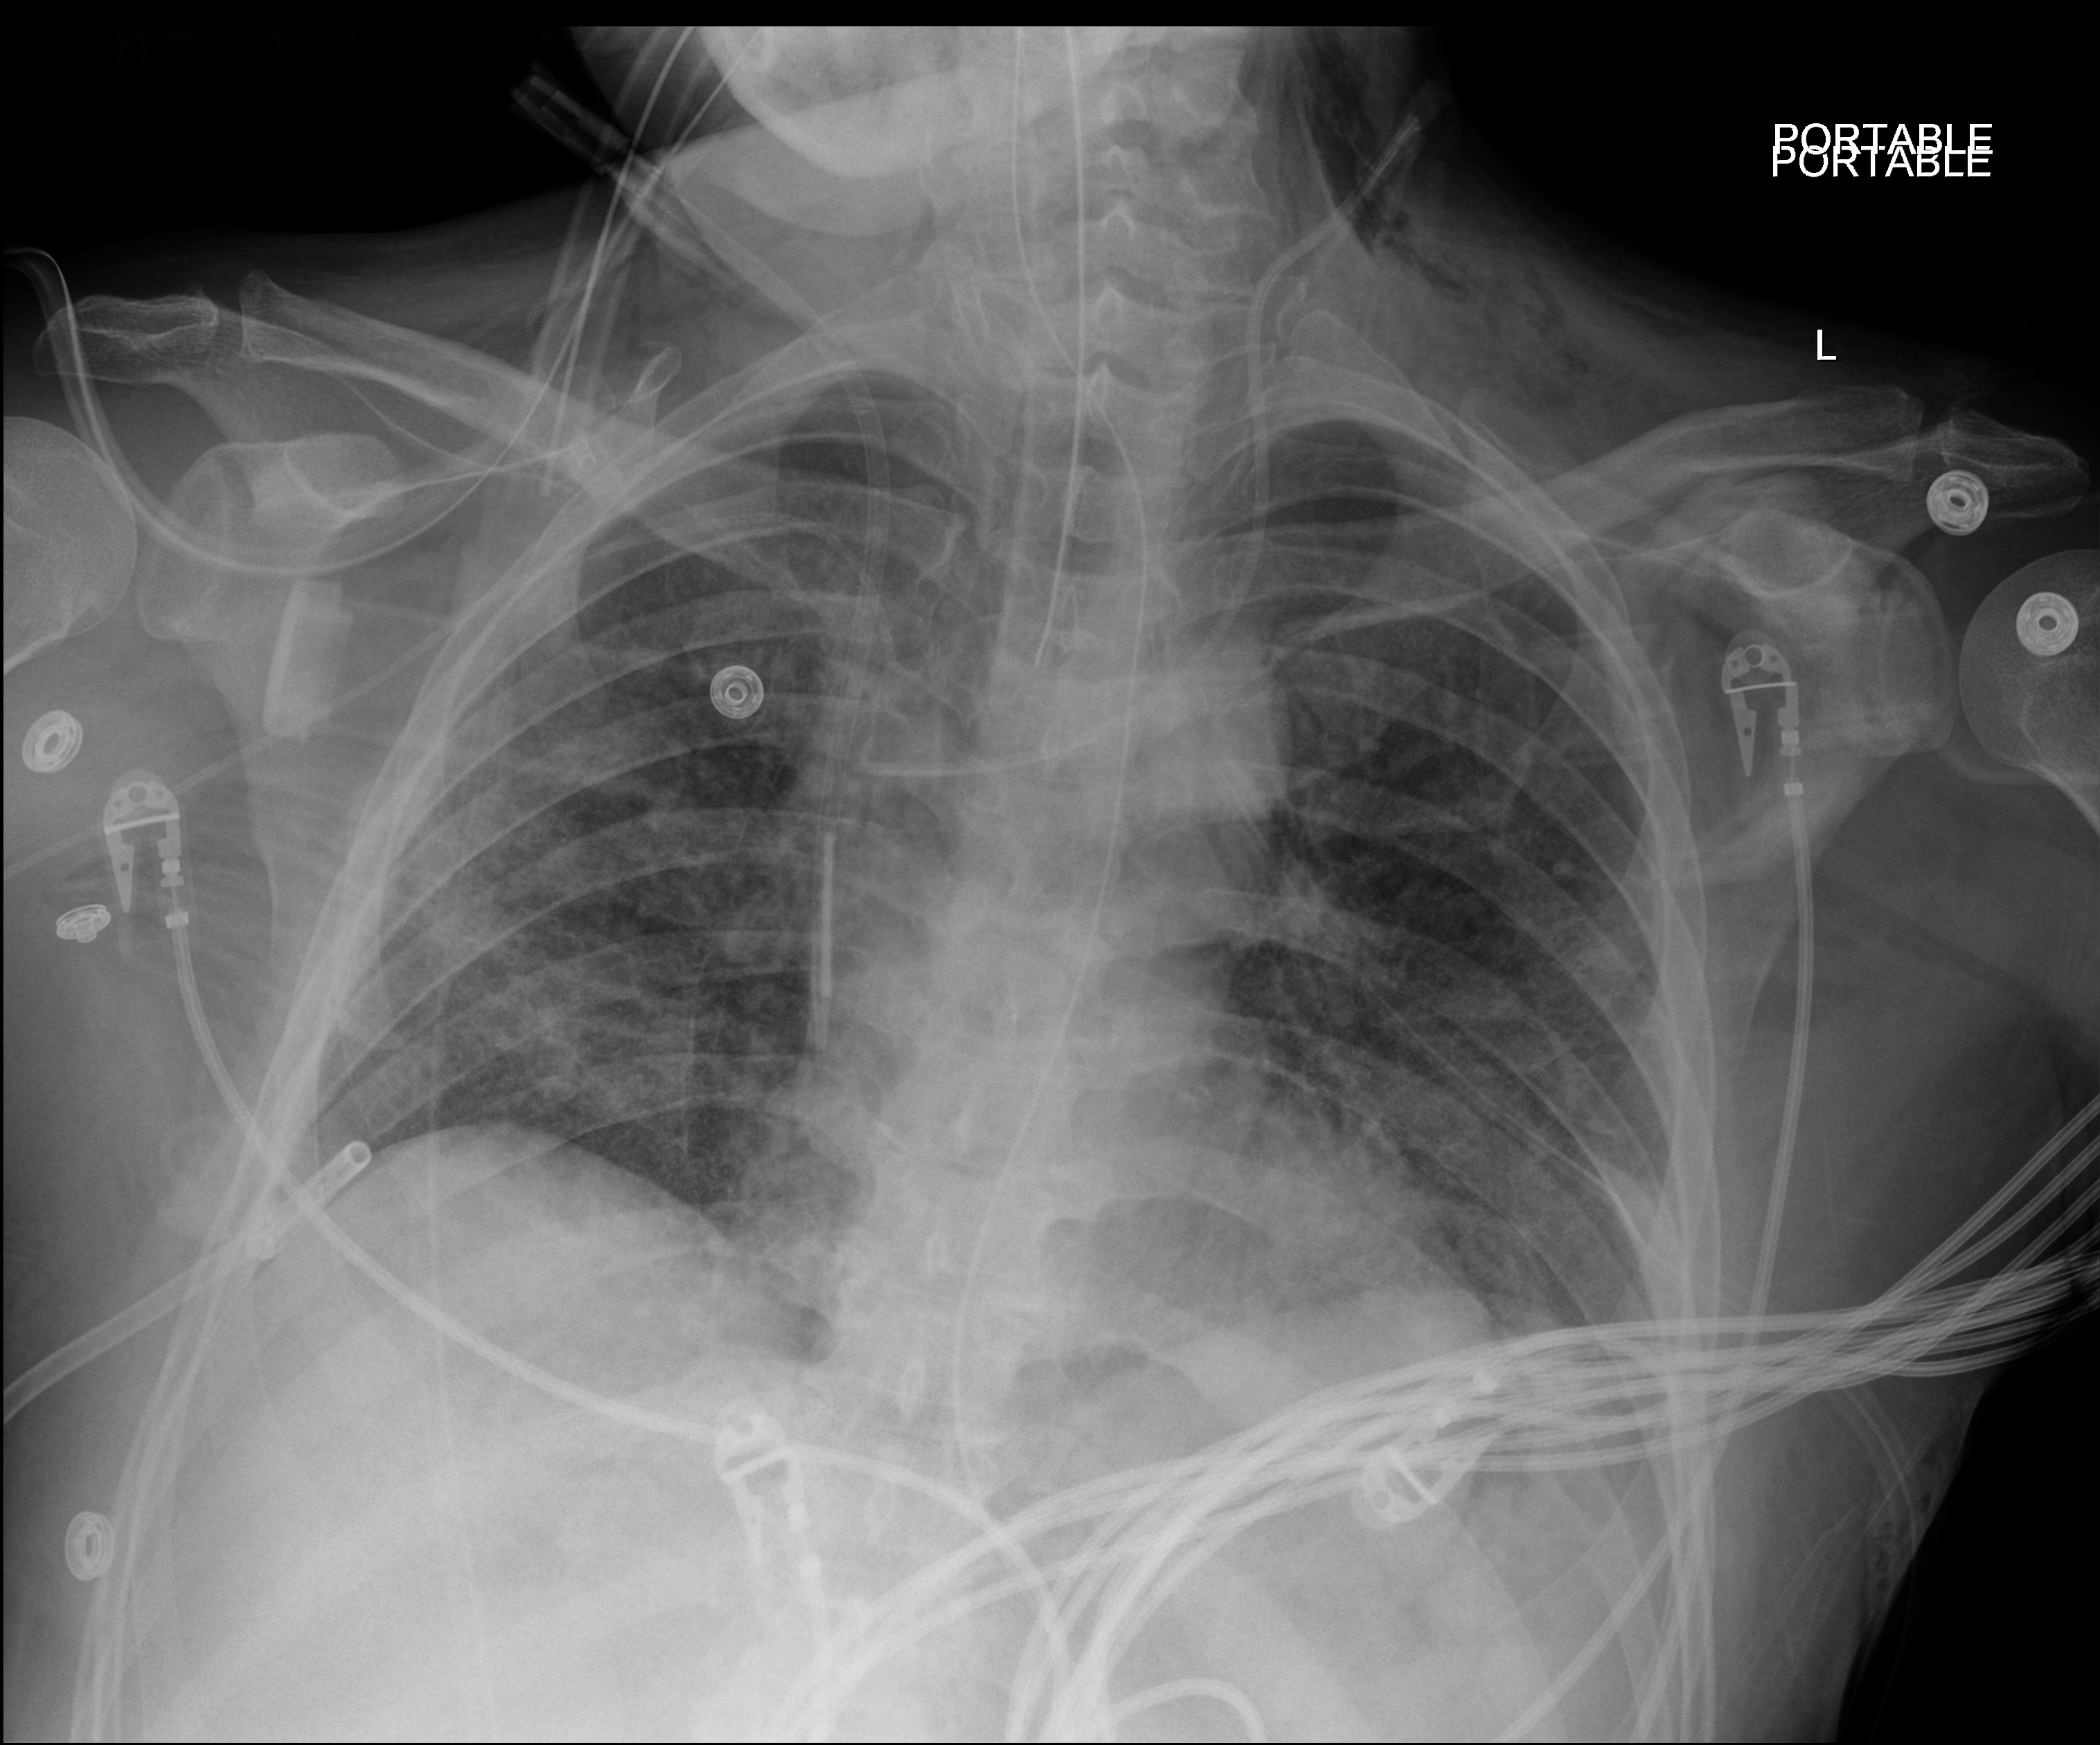
Bedside chest radiograph (digital radiography). Male patient hospitalised with COVID-19, age 18–59 years.
Hospital-stay facts (about this admission, not read from this image; timing relative to this image not recorded): admitted to intensive care during this hospital stay: yes.